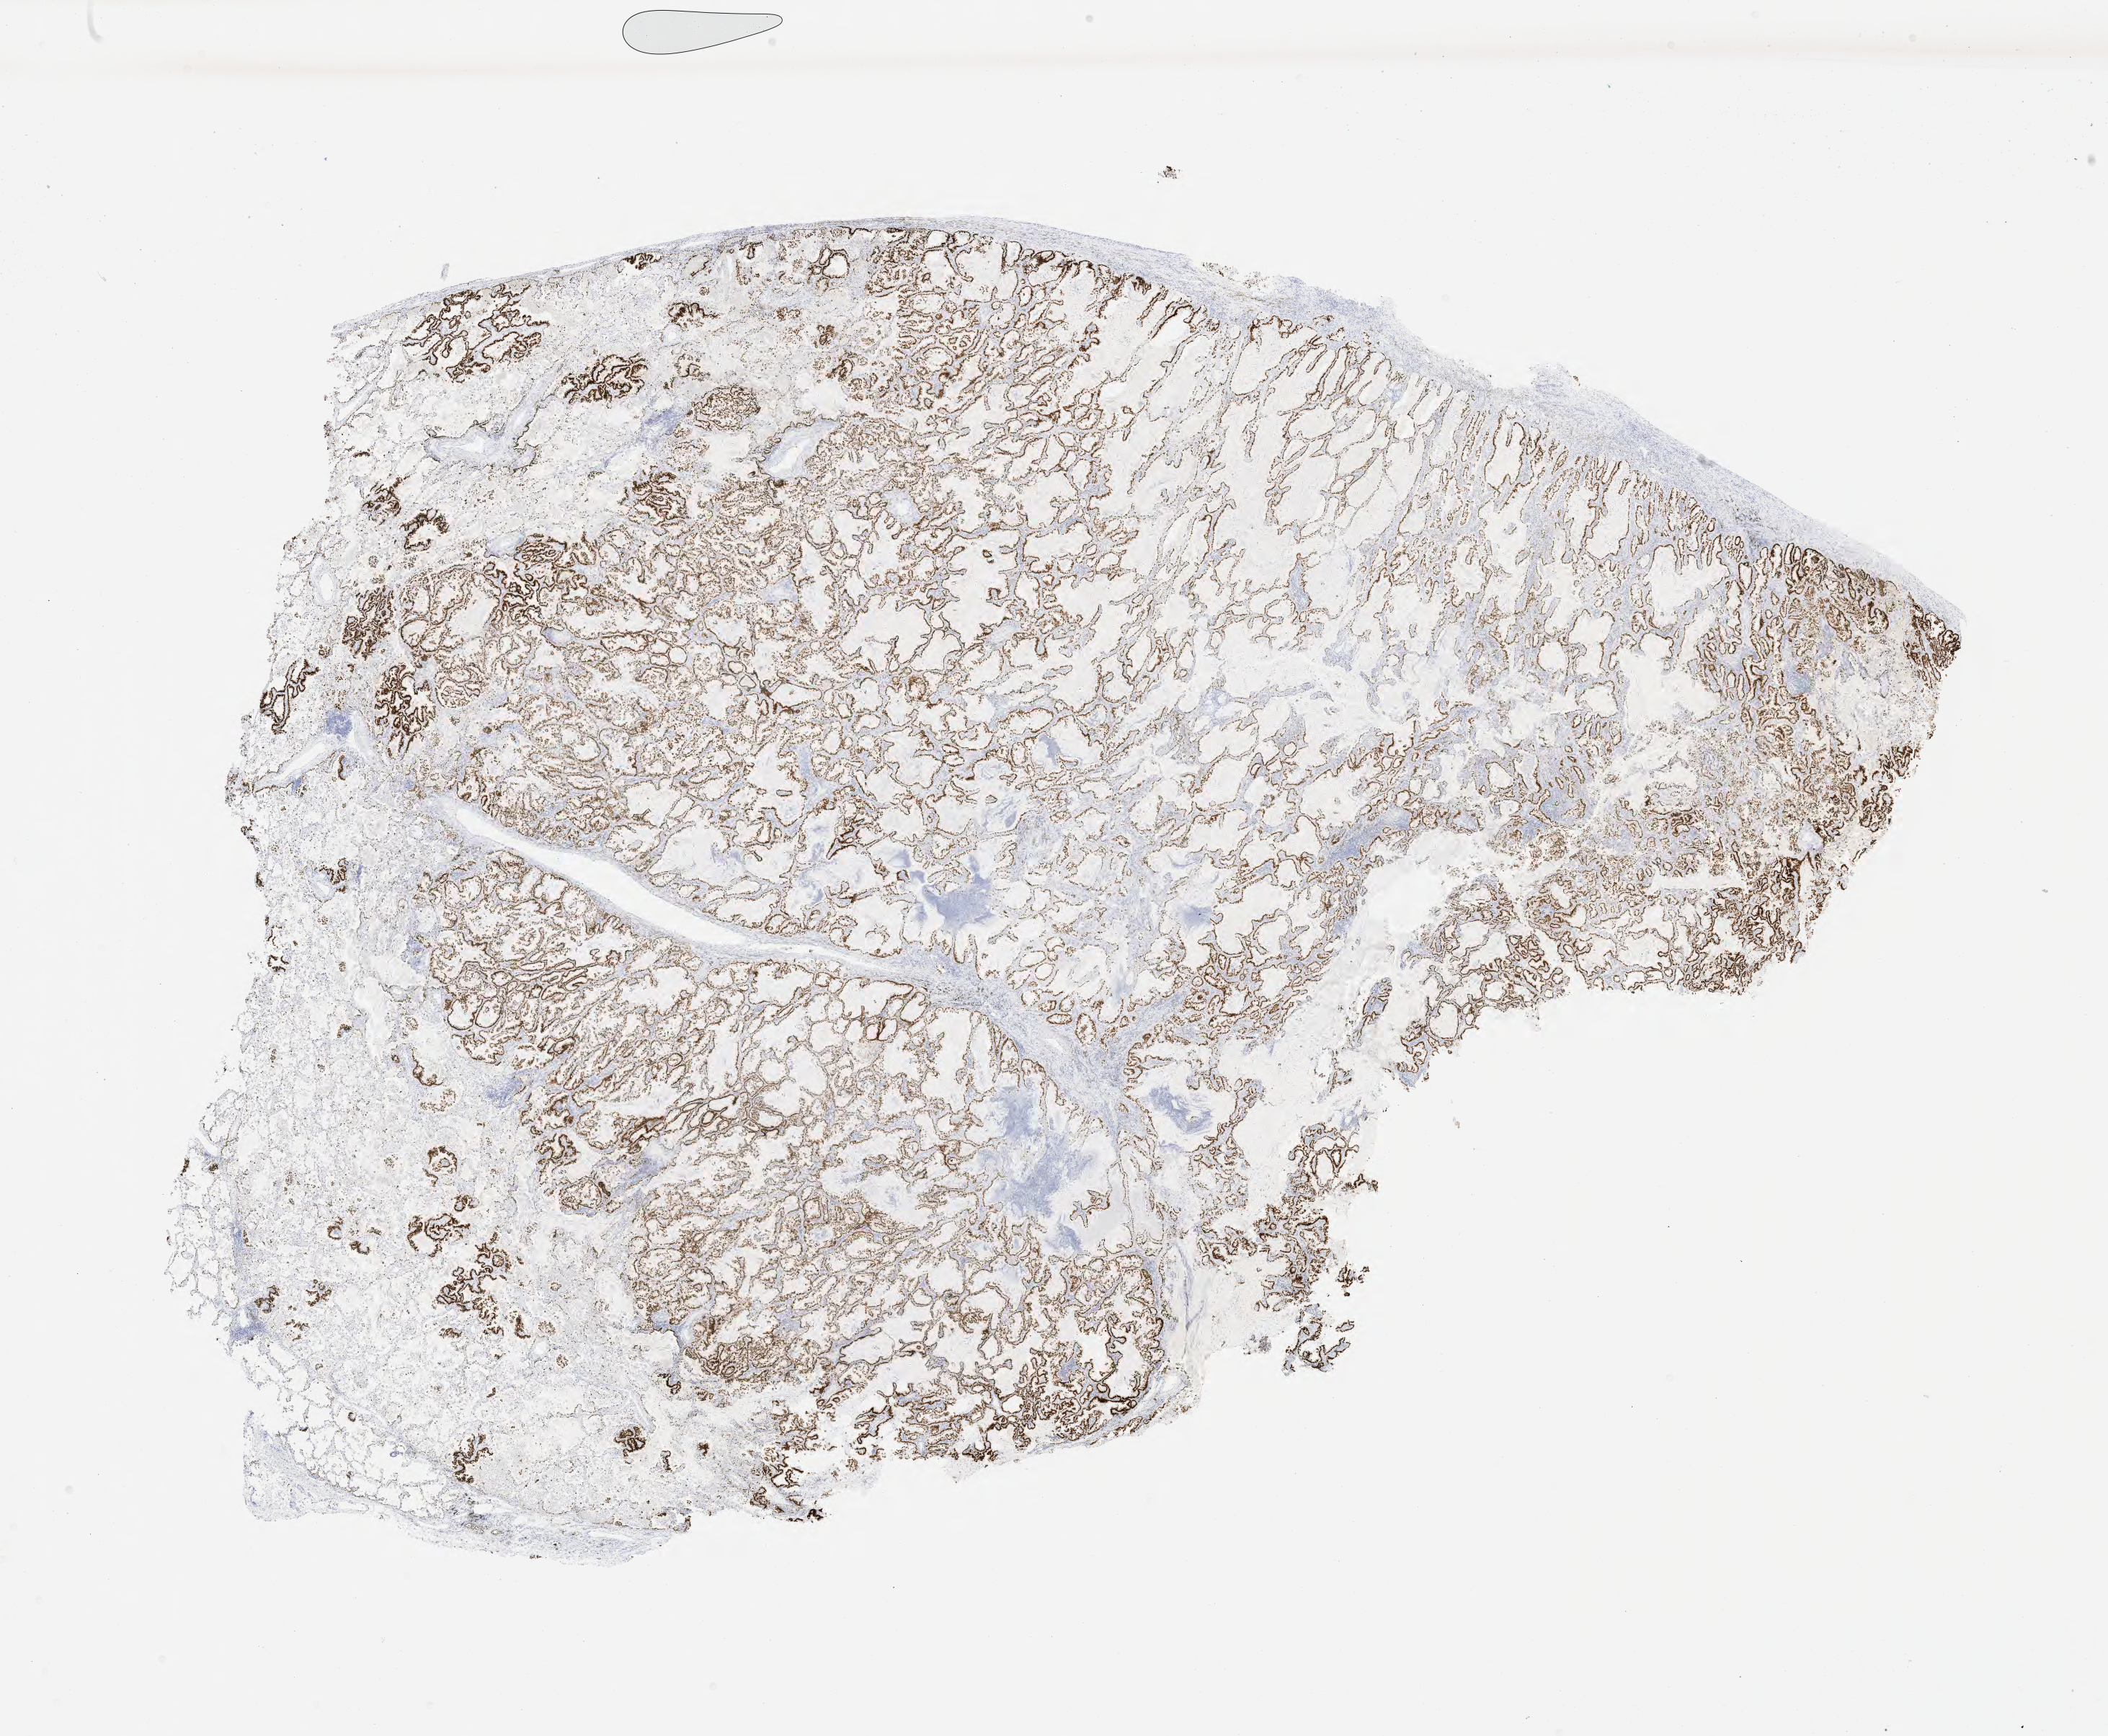
Whole-slide image, immunohistochemical stain for TTF-1 (thyroid transcription factor 1) — shown as a low-resolution overview of the whole scanned area (about 23.6 x 19.5 mm), tumor tissue, site: lung. Male patient.
Histologic diagnosis: Adenocarcinoma, NOS.